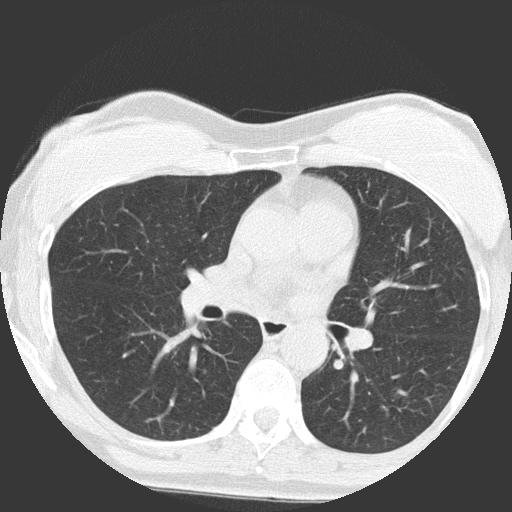
Axial slice from a low-dose chest CT screening exam, baseline annual screen, lung window (W 1500 / L -600 HU), 2 mm slice thickness, slice 67 of 149 in the series, 512 × 512 image matrix, field of view 300 × 300 mm. Female, age 64 years at enrolment. Former smoker at enrolment.
Lesion marked by an expert reader, bounding box [x1, y1, x2, y2] px = [358, 371, 442, 448]. The exam's reader record, not a measurement of the box and not confirmed to be the same lesion: non-calcified nodule or mass ≥4 mm, right upper lobe, 4 × 4 mm, poorly defined margins, ground glass attenuation. Note: the box lies in the patient's left hemithorax on this image, whereas the reader's record names the right lung; they may be different findings. Official screen result: positive, change unspecified: nodule(s) >= 4 mm or enlarging nodule(s), mass(es), or other non-specific abnormalities suspicious for lung cancer. Later outcome: lung cancer diagnosed 932 days after this screen (after the third annual screen) — adenocarcinoma, NOS, left lower lobe, moderately differentiated (G2), stage IA (AJCC 6th edition), 17 mm at pathology.